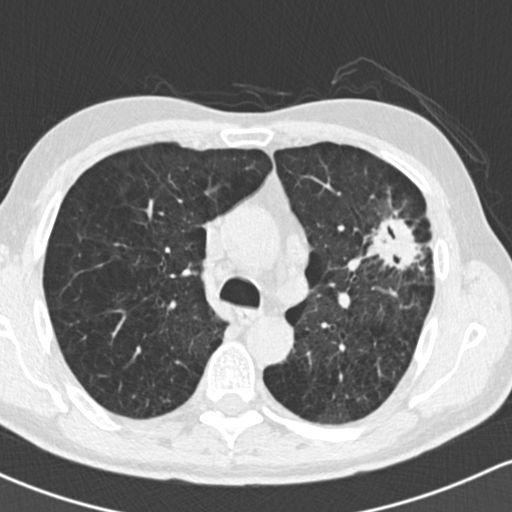
Low-dose screening chest CT, one axial slice; slice 105 of 162 in the series (ordered by position); 120 kVp; lung window (W 1500 / L -600 HU); 2 mm slice thickness; 512 × 512 image matrix, field of view 318 × 318 mm.
Annotated regions visible in this slice (expert manual segmentation):
- lesion 1 (tumor, upper lobe of left lung): bounding box <365,217,424,271> (left, top, right, bottom; pixels)